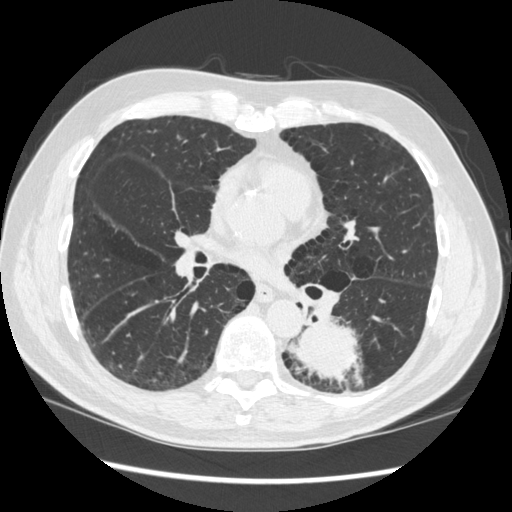
Low-dose screening chest CT, one axial slice. Slice 161 of 348 in the series (ordered by position). 120 kVp. Lung window (W 1500 / L -600 HU). 1.25 mm slice thickness. 512 × 512 image matrix.
Outlined on this slice (manually delineated by an expert):
- lesion 1 (tumor, lower lobe of left lung): bounding box (x1, y1, x2, y2) in pixels: (289, 321, 363, 387)